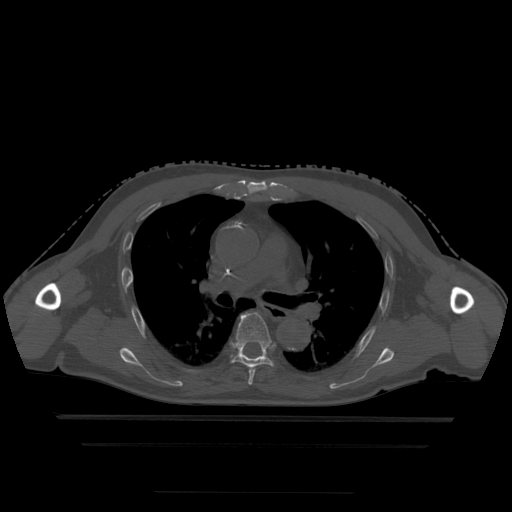
CT including the spine, one axial slice. Slice 320 of 522 in the series (ordered by position). Bone window (W 1800 / L 400 HU). 1.25 mm slice thickness. 512 × 512 image matrix. Patient age 68 years. Case-level facts recorded for this patient, not image findings: primary cancer: urothelial.
Structures marked on this image (semi-automatic segmentation, software-assisted and operator-edited):
- T5 vertebra: bounding box [x1, y1, x2, y2] px = [248, 369, 255, 386]
- T6 vertebra: [232, 313, 273, 370]